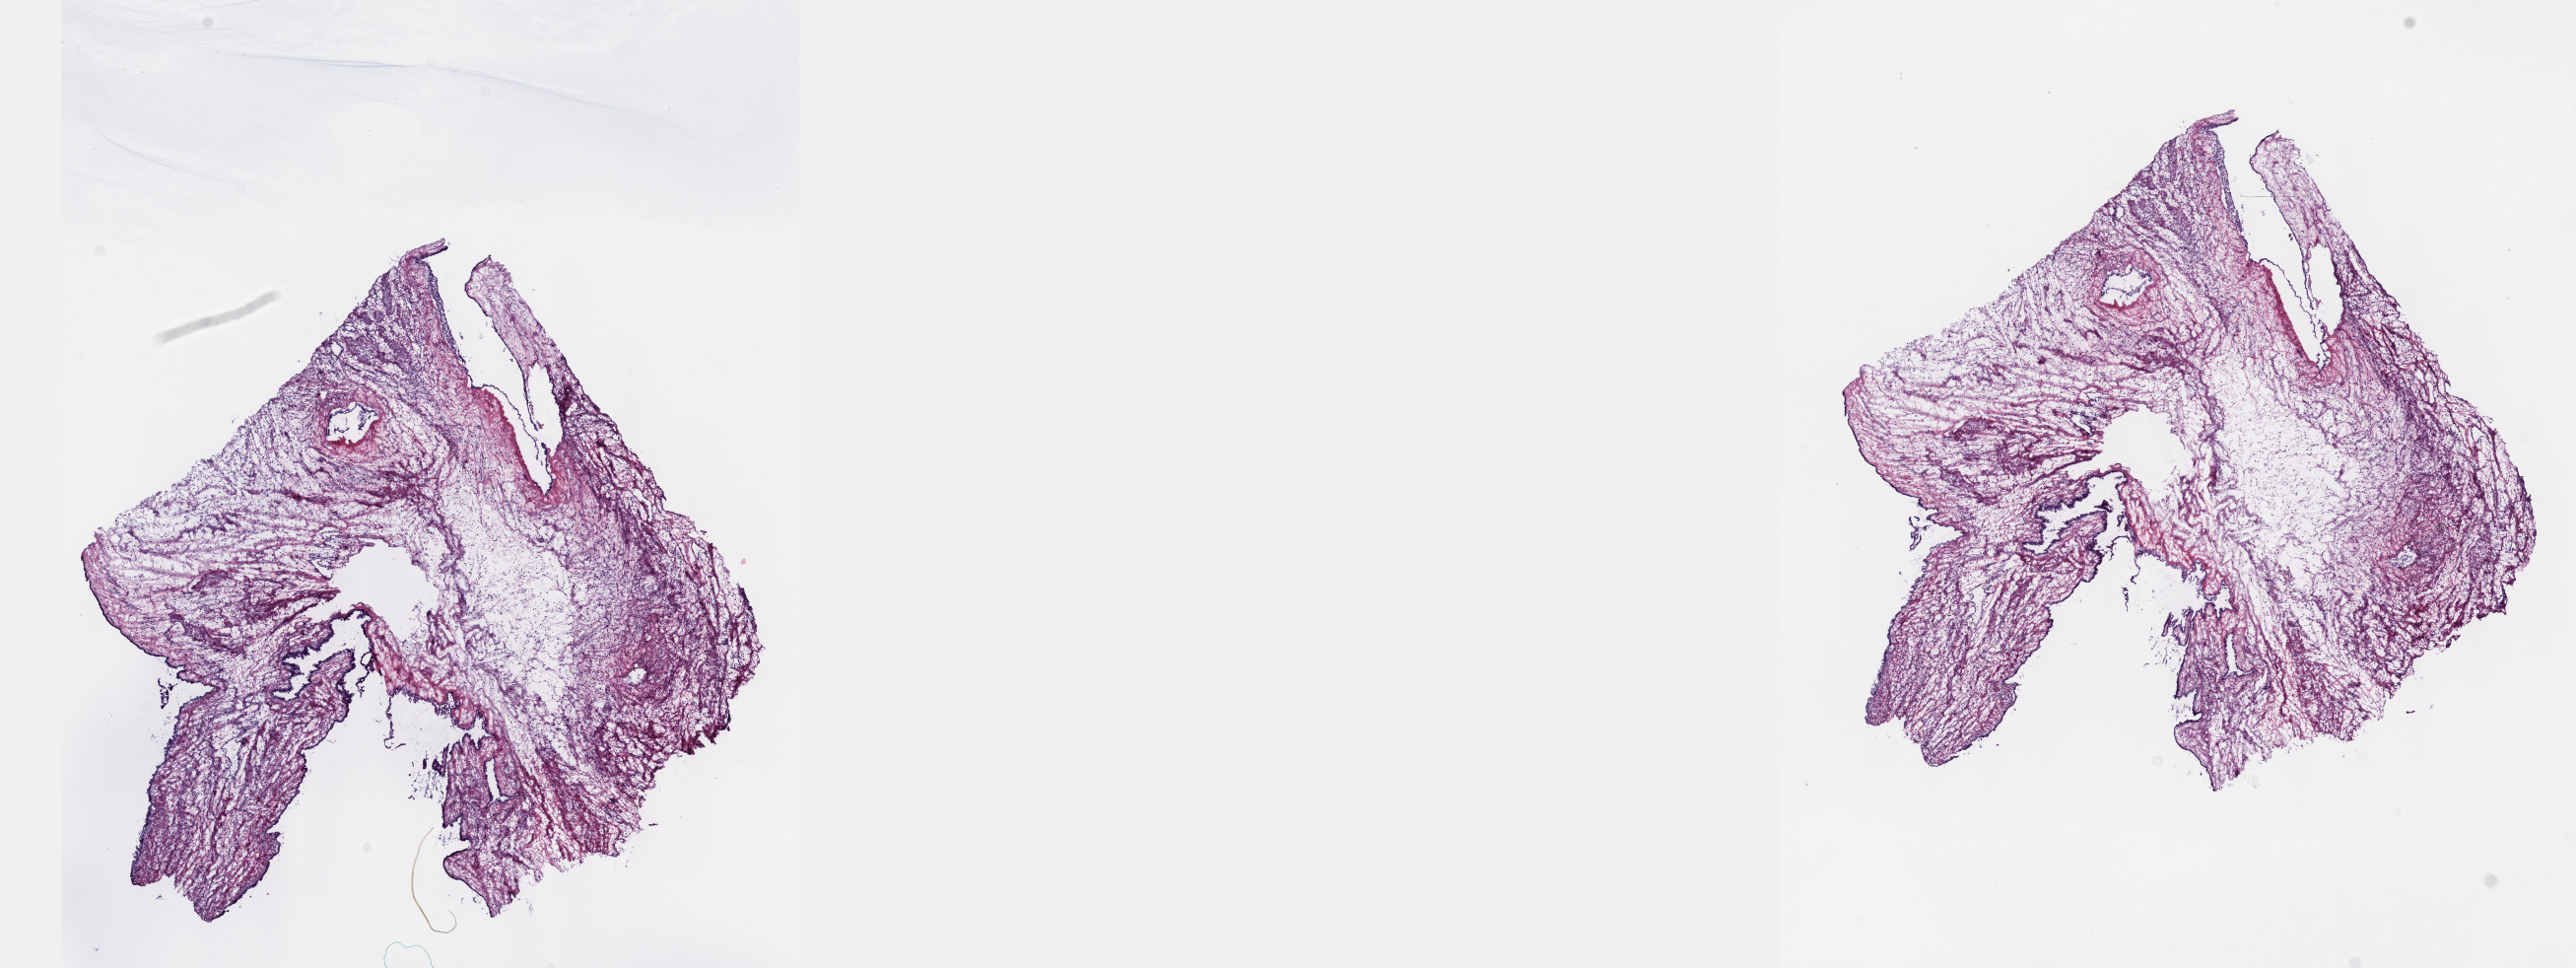
Whole-slide histology image, H&E-stained, shown as a low-resolution overview of the whole scanned area (about 21.1 x 7.9 mm, slide scanned at 40x). Patient sex: male. Composition of this section per pathologist review: tumour cells 100%, tumour nuclei 75%, normal cells 0%, stromal cells 0%, necrosis 0%. Inflammatory infiltration, as recorded: lymphocyte infiltration 2%, monocyte infiltration 0%, neutrophil infiltration 0%.
- specimen: frozen section; testis, primary tumour sample